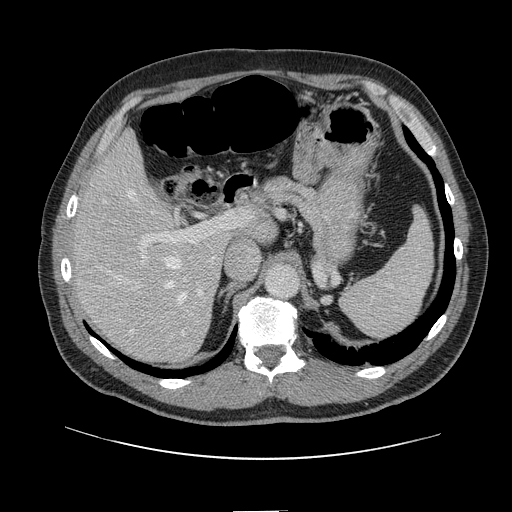
Contrast-enhanced abdominal CT, one axial slice. Position 88 of 161 along the scan axis. 120 kVp. Intravenous contrast given. Soft-tissue window (W 400 / L 40 HU). 2.5 mm slice thickness. 512 × 512 image matrix, field of view 412 × 412 mm. Male patient, age 66 years. Case-level facts recorded for this patient, not image findings: diagnosis: colorectal cancer liver metastases, imaged before liver resection; multiple liver metastases: no; largest metastasis: 3.5 cm; chemotherapy before resection: yes.
Annotated regions visible in this slice (outlined manually by an expert reader):
- hepatic veins: bounding box [x1, y1, x2, y2] px = [103, 188, 187, 333]
- liver: [76, 137, 273, 361]
- planned liver remnant (the part of the liver to remain after resection): [76, 137, 273, 305]
- portal vein (with intrahepatic branches): [138, 212, 240, 314]